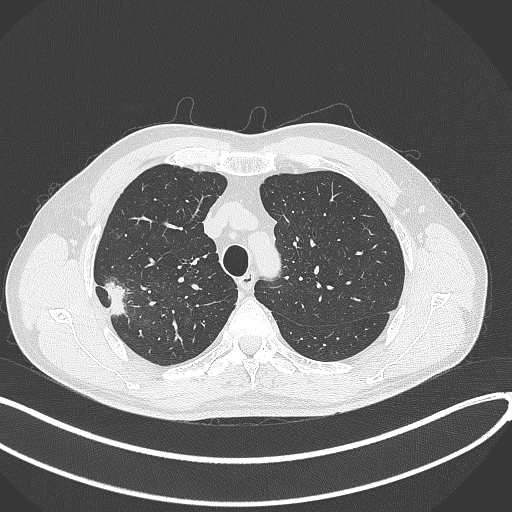
Chest CT, one axial slice; slice 325 of 381 in the series (ordered by position); reconstruction kernel B70f; 120 kVp; lung window (W 1500 / L -600 HU); 1 mm slice thickness; 512 × 512 image matrix, field of view 400 × 400 mm. Patient: male, 62 years. From the clinical record (not read from this slice): clinical TNM (as recorded): T1c N0 M0; histopathological grade: G2-3.
Structures marked on this image (rectangle marked by the reading radiologist):
- lung tumour (recorded histology: adenocarcinoma): box from (x=101, y=278) to (x=127, y=318) px